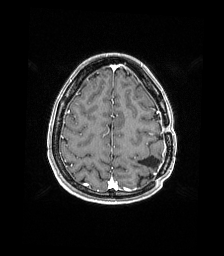
Brain MRI from a brain-tumour surgery series, one axial slice; position 49 of 176 along the scan axis; T1-weighted post-contrast; 1 mm slice thickness; 224 × 256 image matrix, field of view 224 × 256 mm. From the clinical record (not read from this slice): histopathology: Atypical meningioma; WHO grade: 2; tumour location: Paramedian Left Parietal.
Outlined on this slice (outlined manually by an expert reader):
- previous resection cavity: bounding box (x1, y1, x2, y2) in pixels: (139, 156, 160, 169)